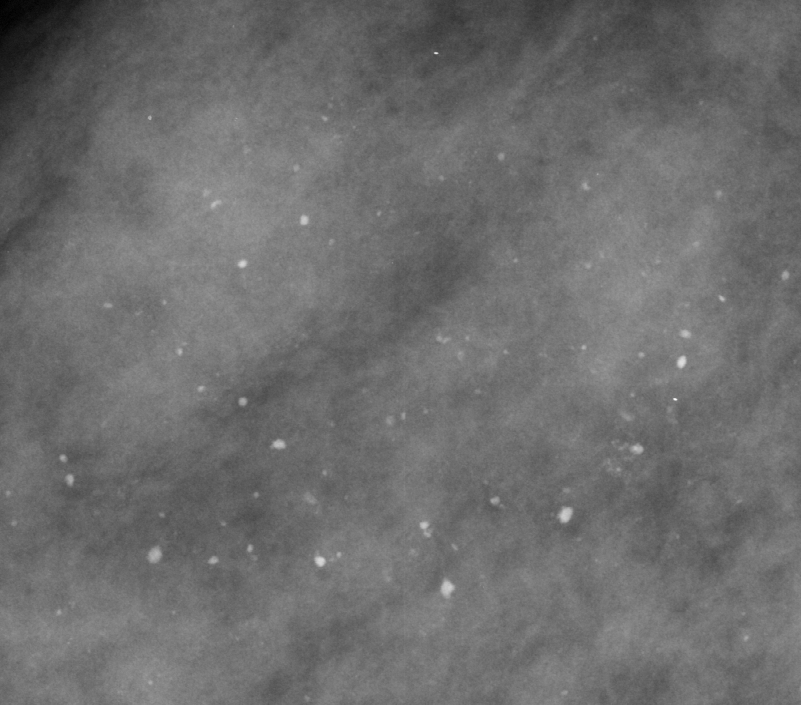
Cropped region of a digitized screen-film mammogram centred on a radiologist-marked abnormality, right breast, MLO view.
- Finding: calcifications, morphology vascular / coarse / lucent center / round and regular / punctate, distribution regional; BI-RADS assessment category 2; benign; no additional work-up was recommended (benign without callback).